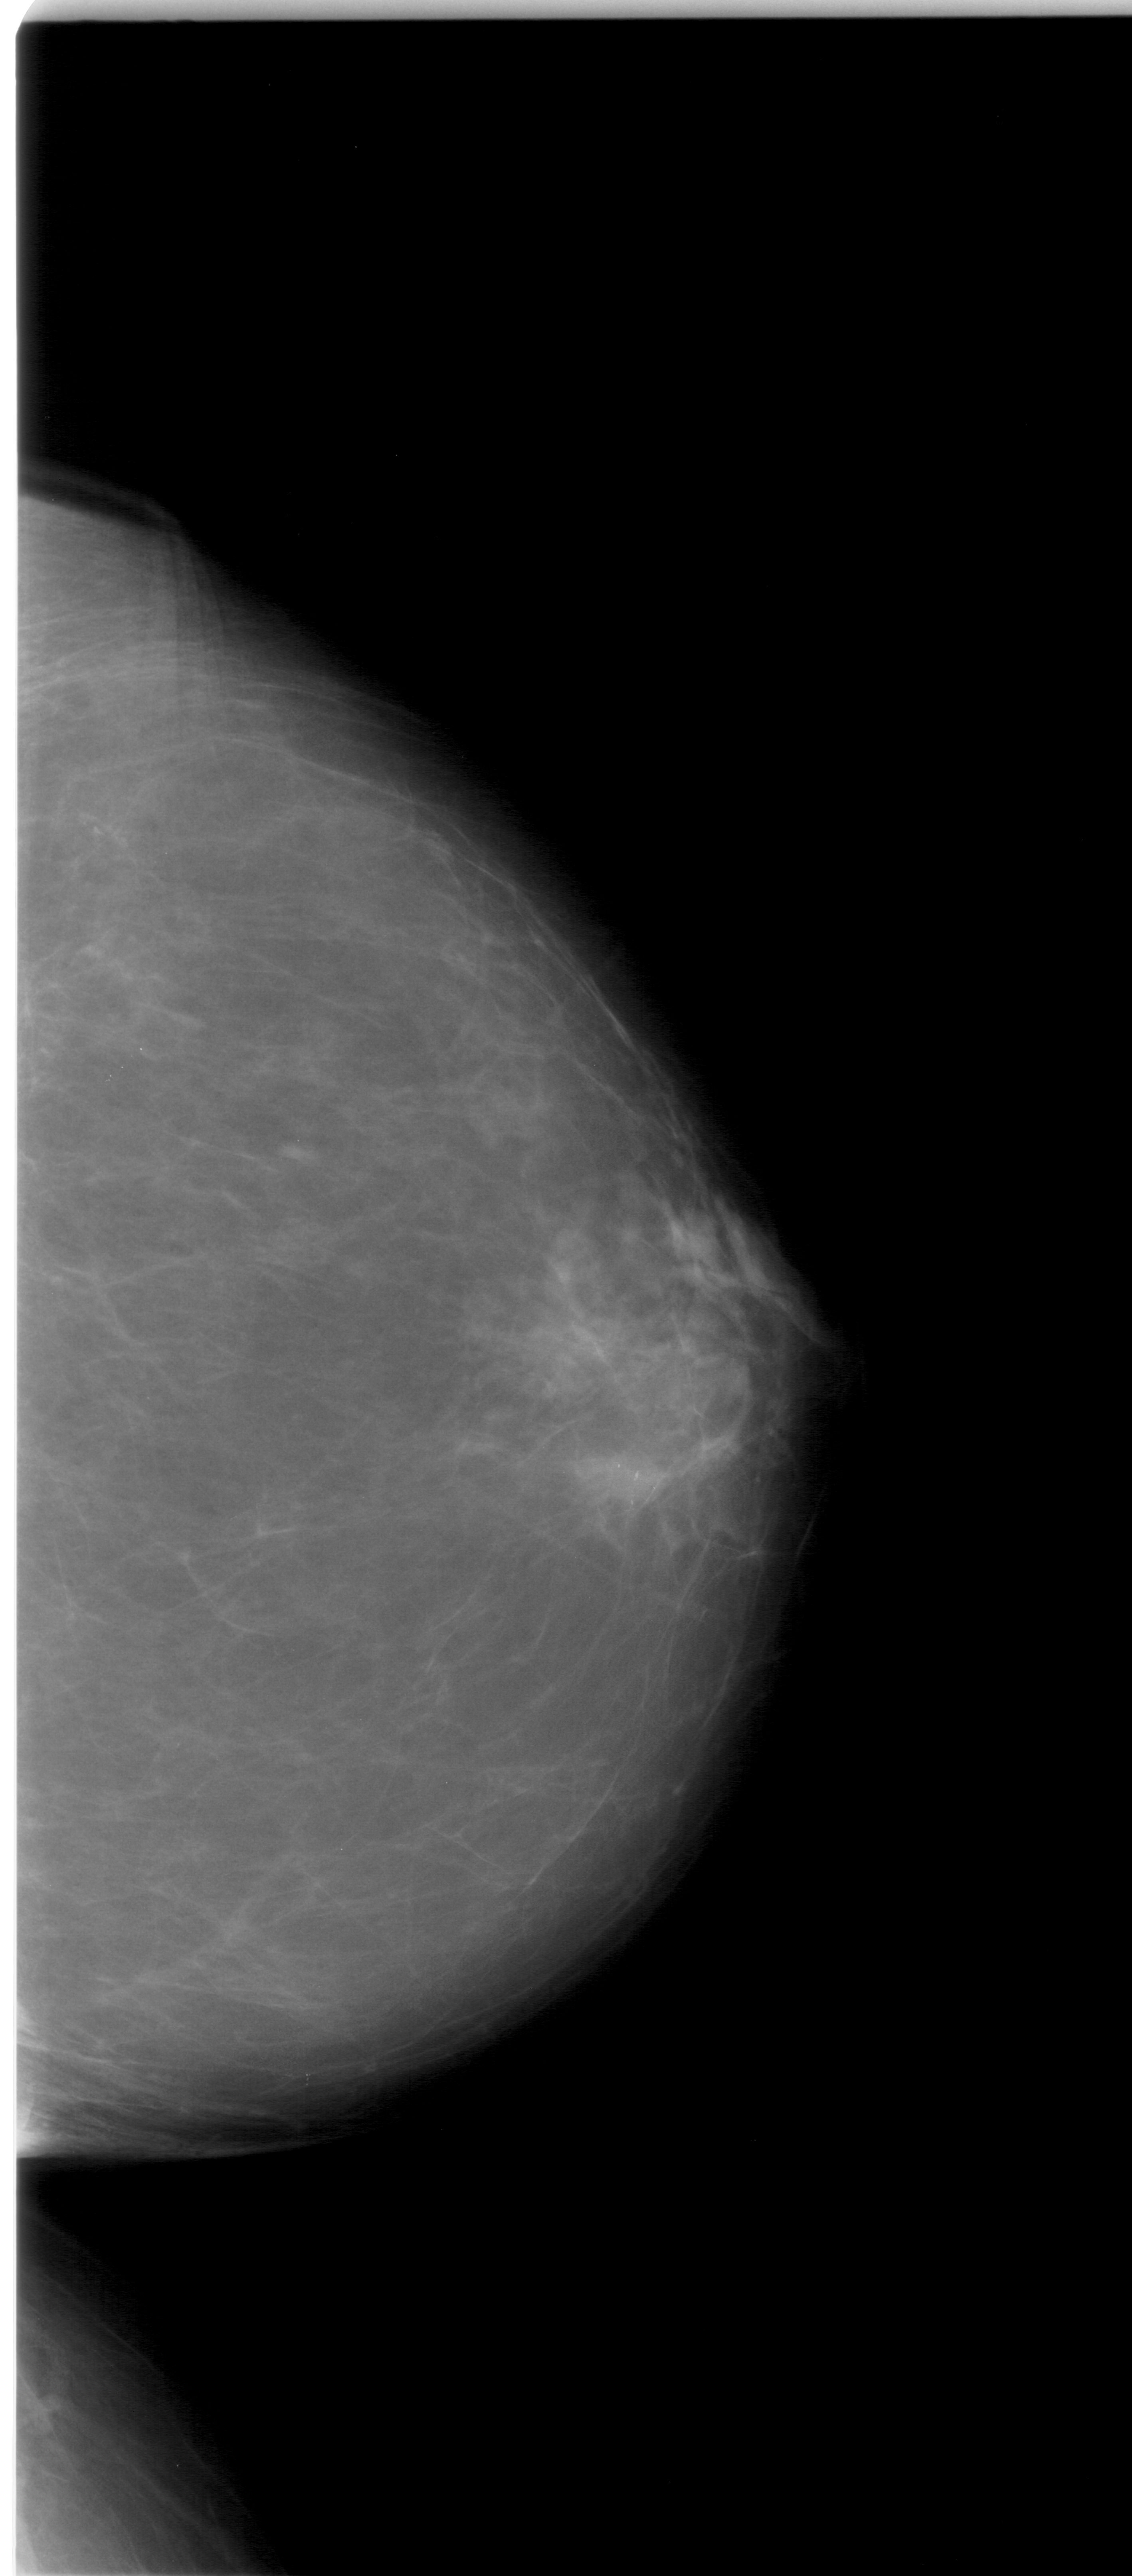
Scanned film-screen mammogram; right breast; craniocaudal (CC) view; 1132 × 2576 image matrix.
Expert-marked regions of interest on this image (one box per marked abnormality):
- calcifications, morphology pleomorphic, distribution clustered; BI-RADS assessment category 4; subtlety rating 3 on a 1 (subtle) to 5 (obvious) scale; pathology result (as recorded, not read from the image): malignant: bounding box <585,1447,686,1510> (left, top, right, bottom; pixels)